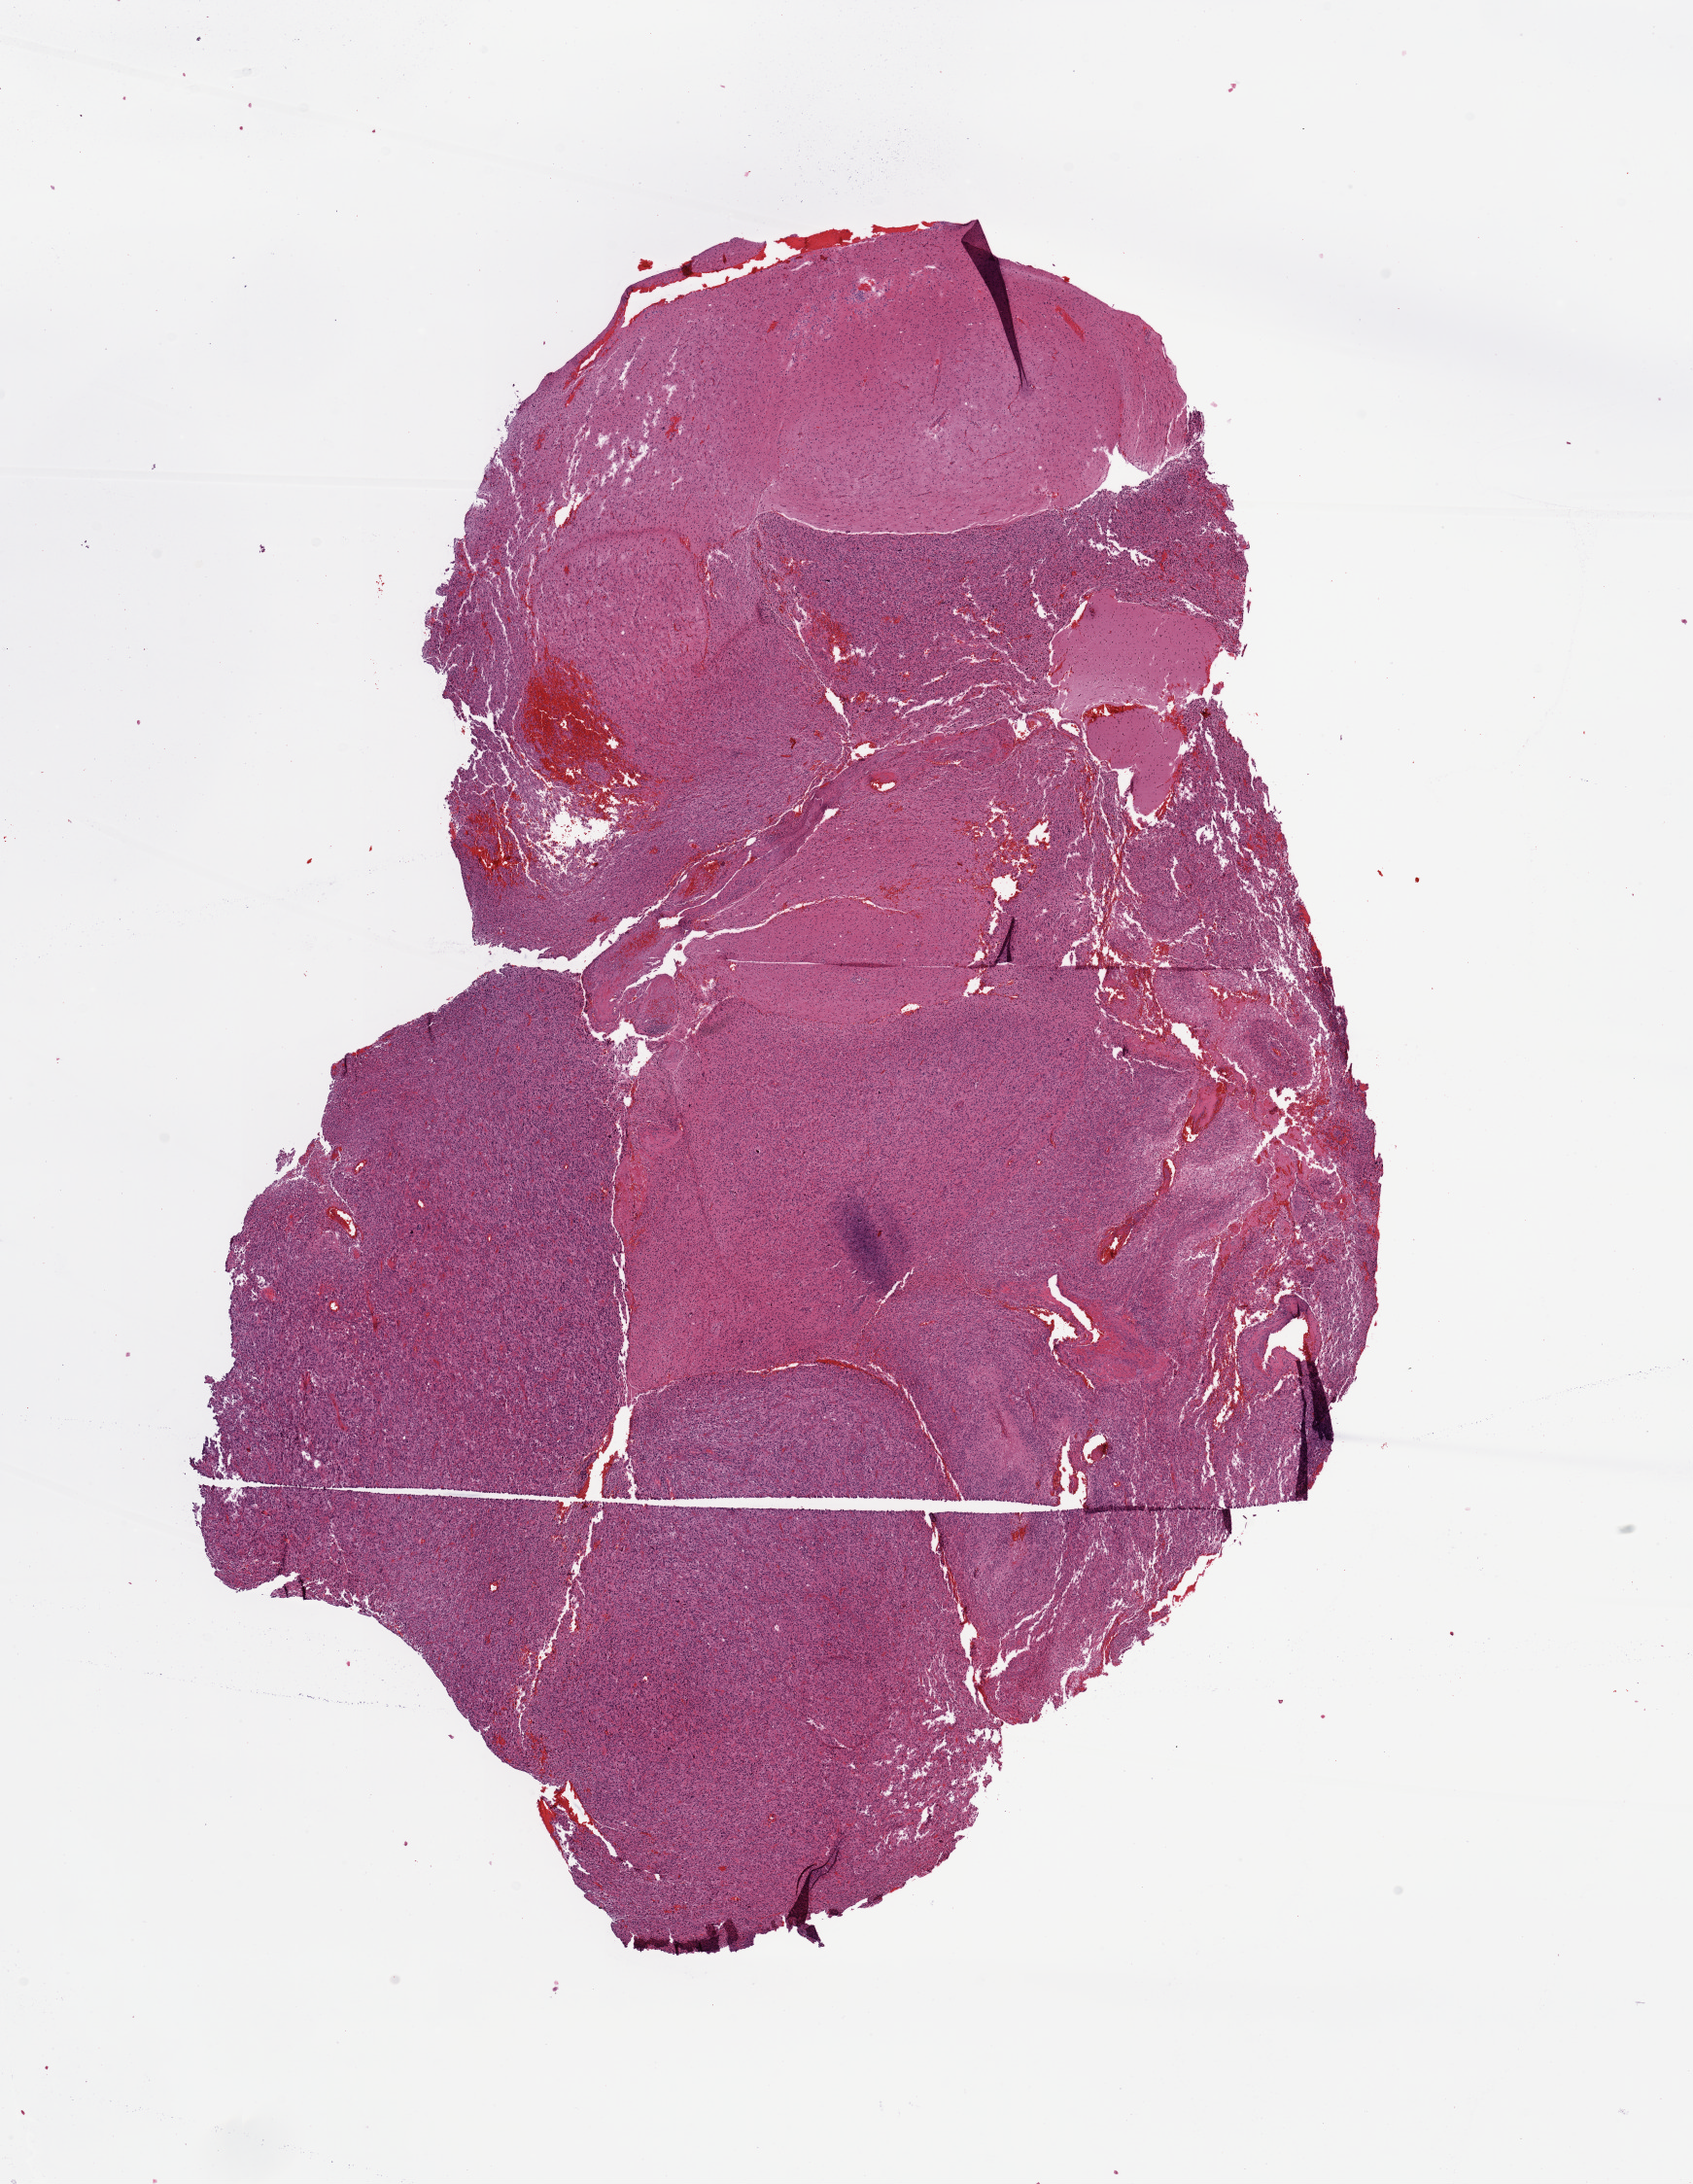
H&E-stained whole-slide image, a low-resolution overview of the entire scanned area, about 13.8 x 17.8 mm, brain, tumour tissue. 58-year-old male patient.
Histologic diagnosis: Glioblastoma. Primary tumour site (as recorded): temporal lobe.